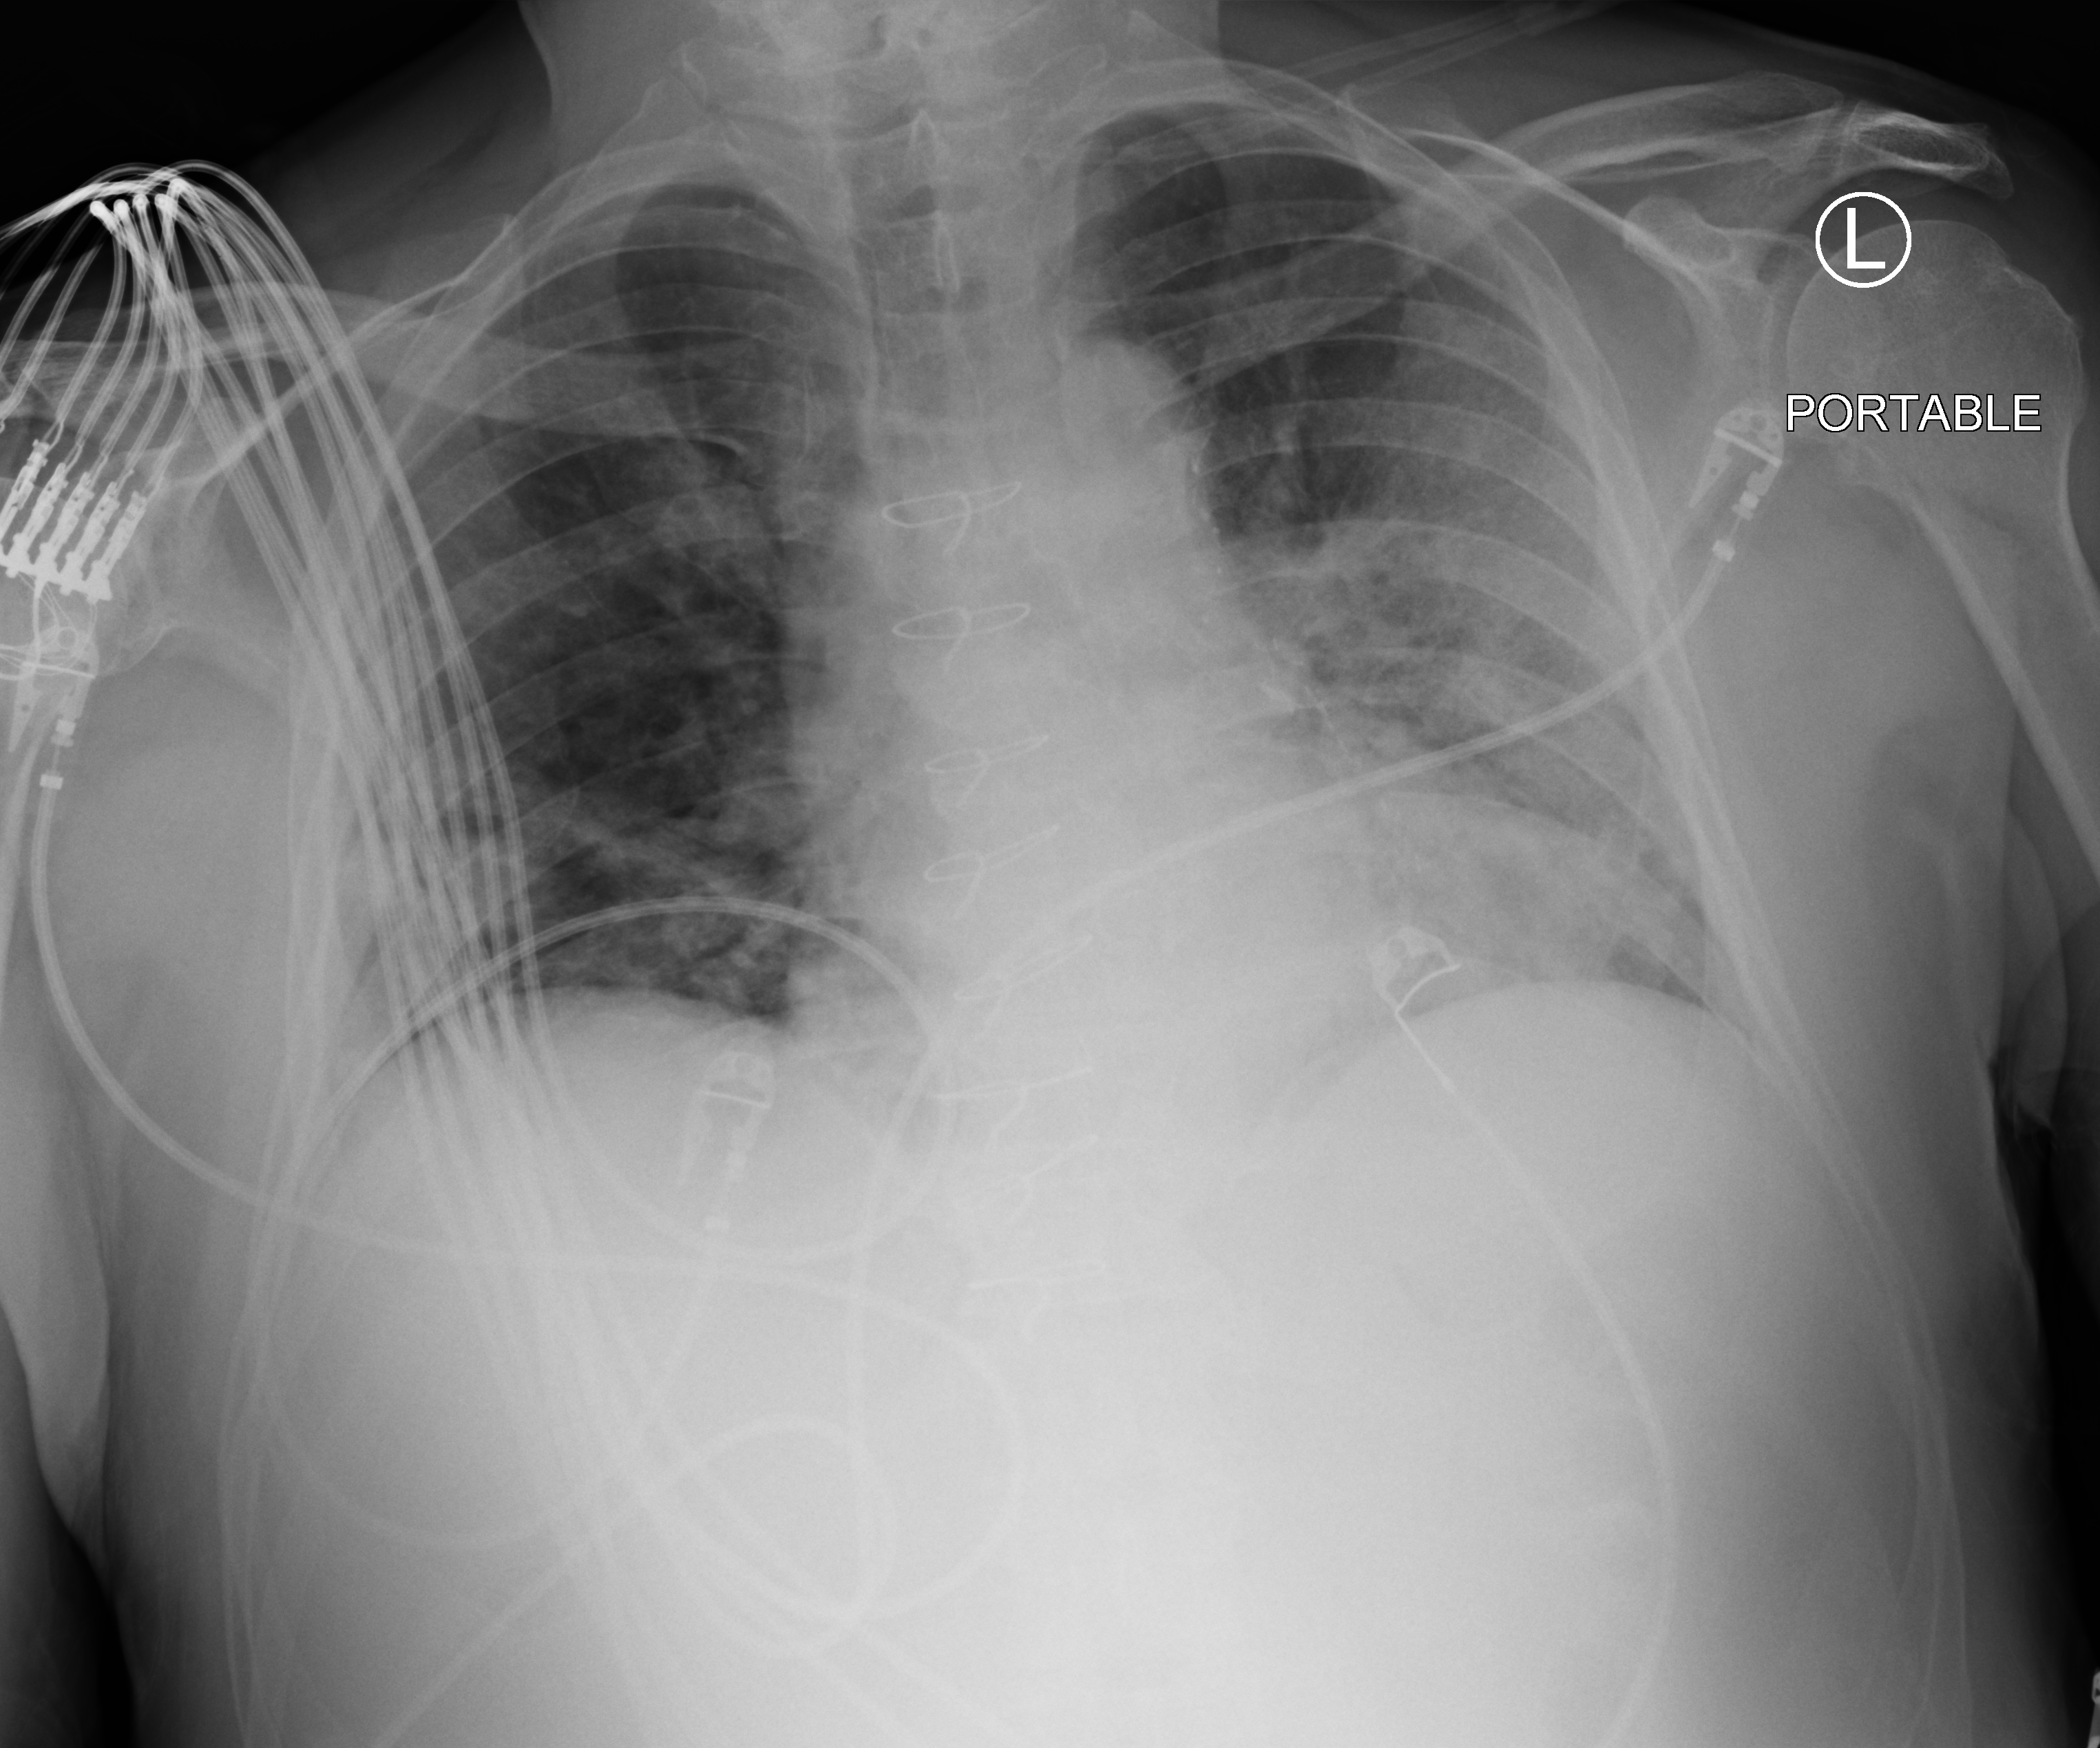
Portable chest radiograph, anteroposterior (AP) projection. Male patient hospitalised with COVID-19, age 60–74 years.
Hospital-stay facts (about this admission, not read from this image; timing relative to this image not recorded): admitted to intensive care during this hospital stay: yes.